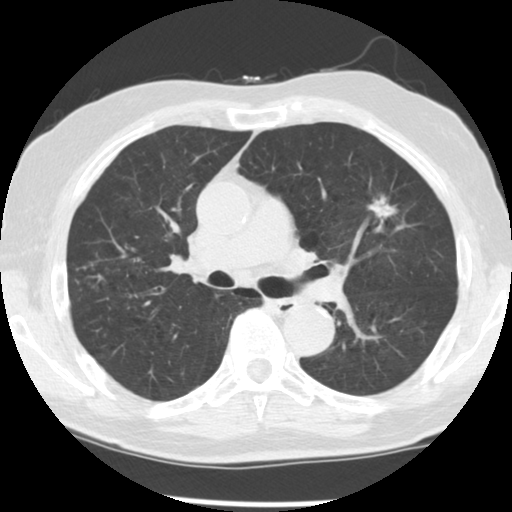
Axial slice from a low-dose chest CT screening exam, third annual screen, lung window (W 1500 / L -600 HU). Male, age 70 years at enrolment.
Lesion marked by an expert reader, bounding box (x1, y1, x2, y2) in pixels: (356, 185, 412, 242). The screening reader recorded 3 non-calcified nodules or masses ≥4 mm on this exam (left upper lobe, left upper lobe, right lower lobe); which of them this box marks is not recorded. Official screen result: positive, other.